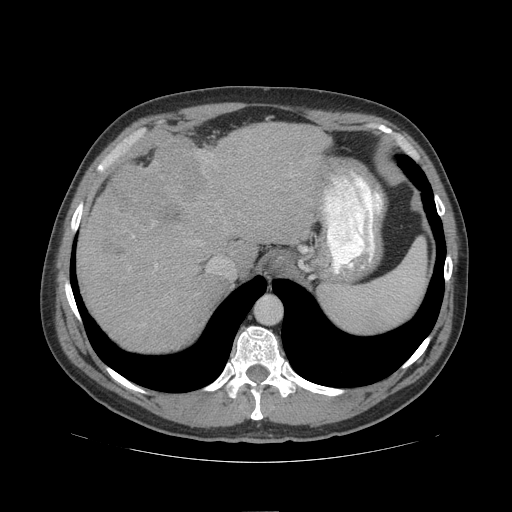
Contrast-enhanced abdominal CT (liver protocol), one axial slice; position 81 of 109 along the scan axis; reconstruction kernel STANDARD; soft-tissue window (W 400 / L 40 HU); 512 × 512 image matrix. Case-level facts recorded for this patient, not image findings: diagnosis: hepatocellular carcinoma (patient treated with transarterial chemoembolisation; whether this scan precedes or follows treatment is not stated here); TNM stage (as recorded): Stage-IIIB; Child-Pugh class: A; tumour differentiation: poorly differentiated.
Outlined on this slice (semi-automatically segmented with operator editing):
- abdominal aorta: box from (x=256, y=297) to (x=282, y=324) px
- liver parenchyma outside the tumour (the mass and vessels are separate outlines, so this box may not span the whole liver): (x=78, y=122)–(x=330, y=352)
- mass: (x=110, y=139)–(x=229, y=239)